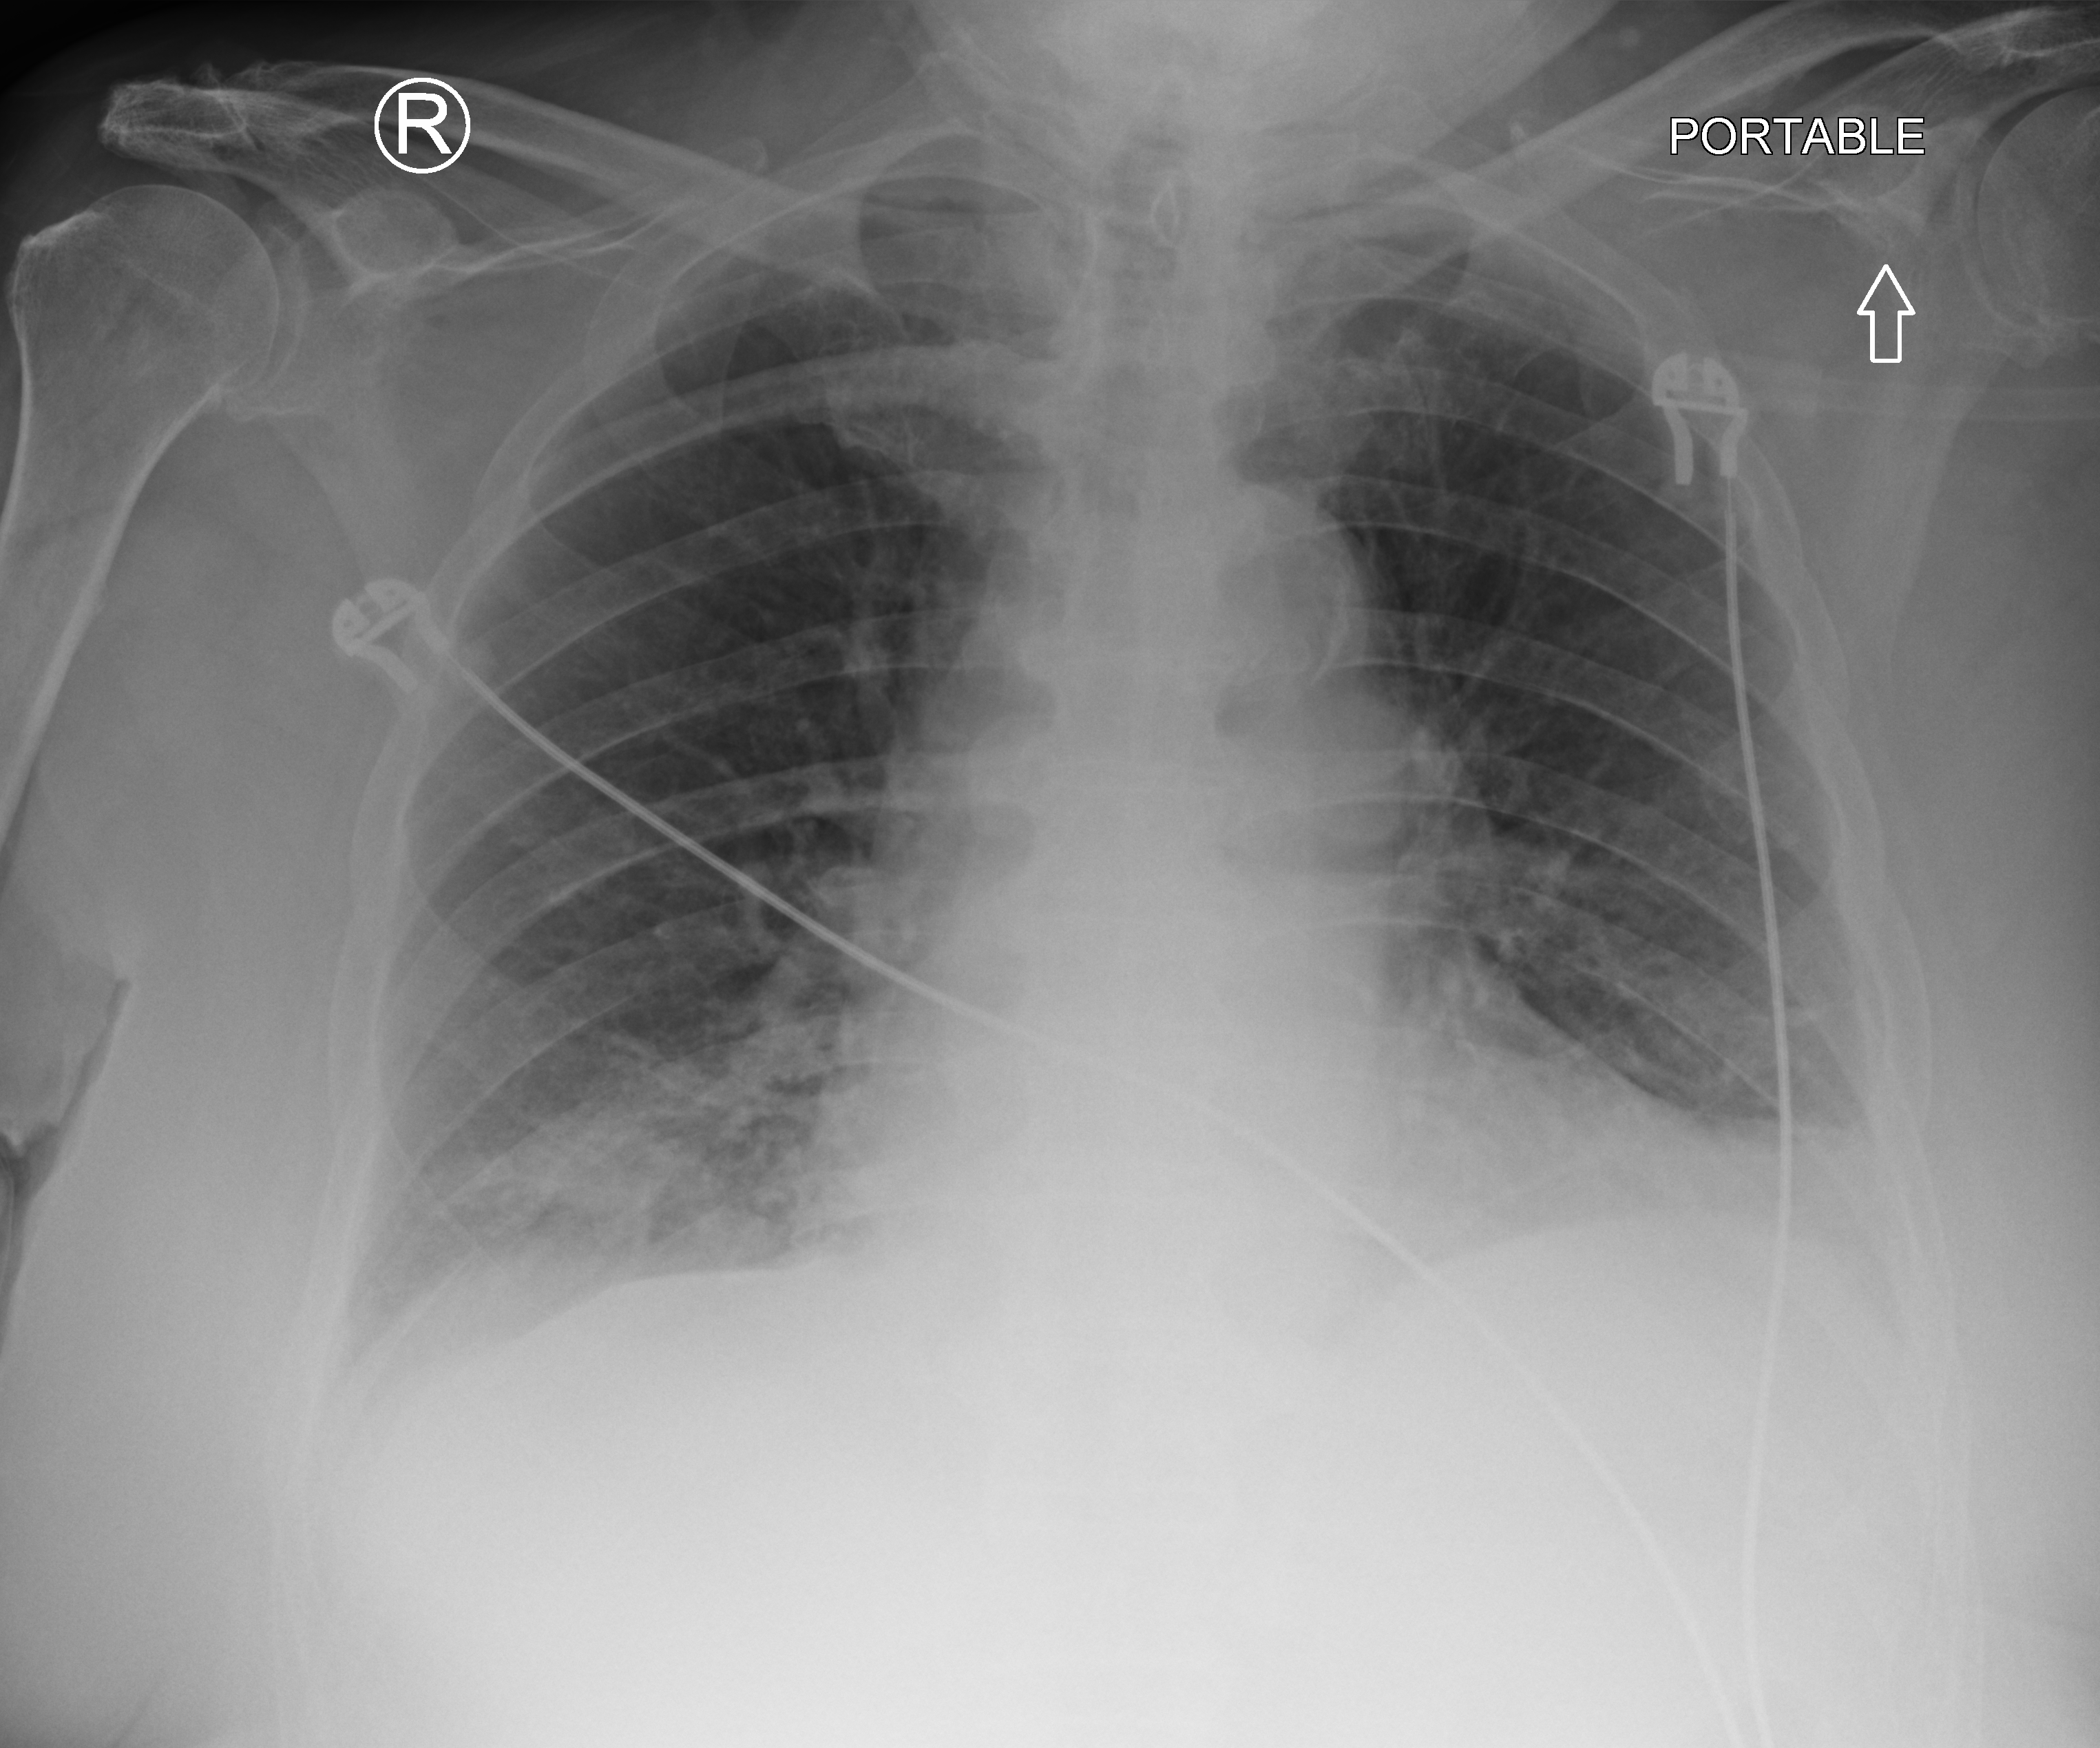
Portable chest radiograph, anteroposterior (AP) projection. Male patient hospitalised with COVID-19, age 75–90 years.
Admission-level facts for this patient (not findings on this image; timing relative to this image not recorded): admitted to intensive care during this hospital stay: no; COPD (admission record): yes; mechanically ventilated during this hospital stay: no.